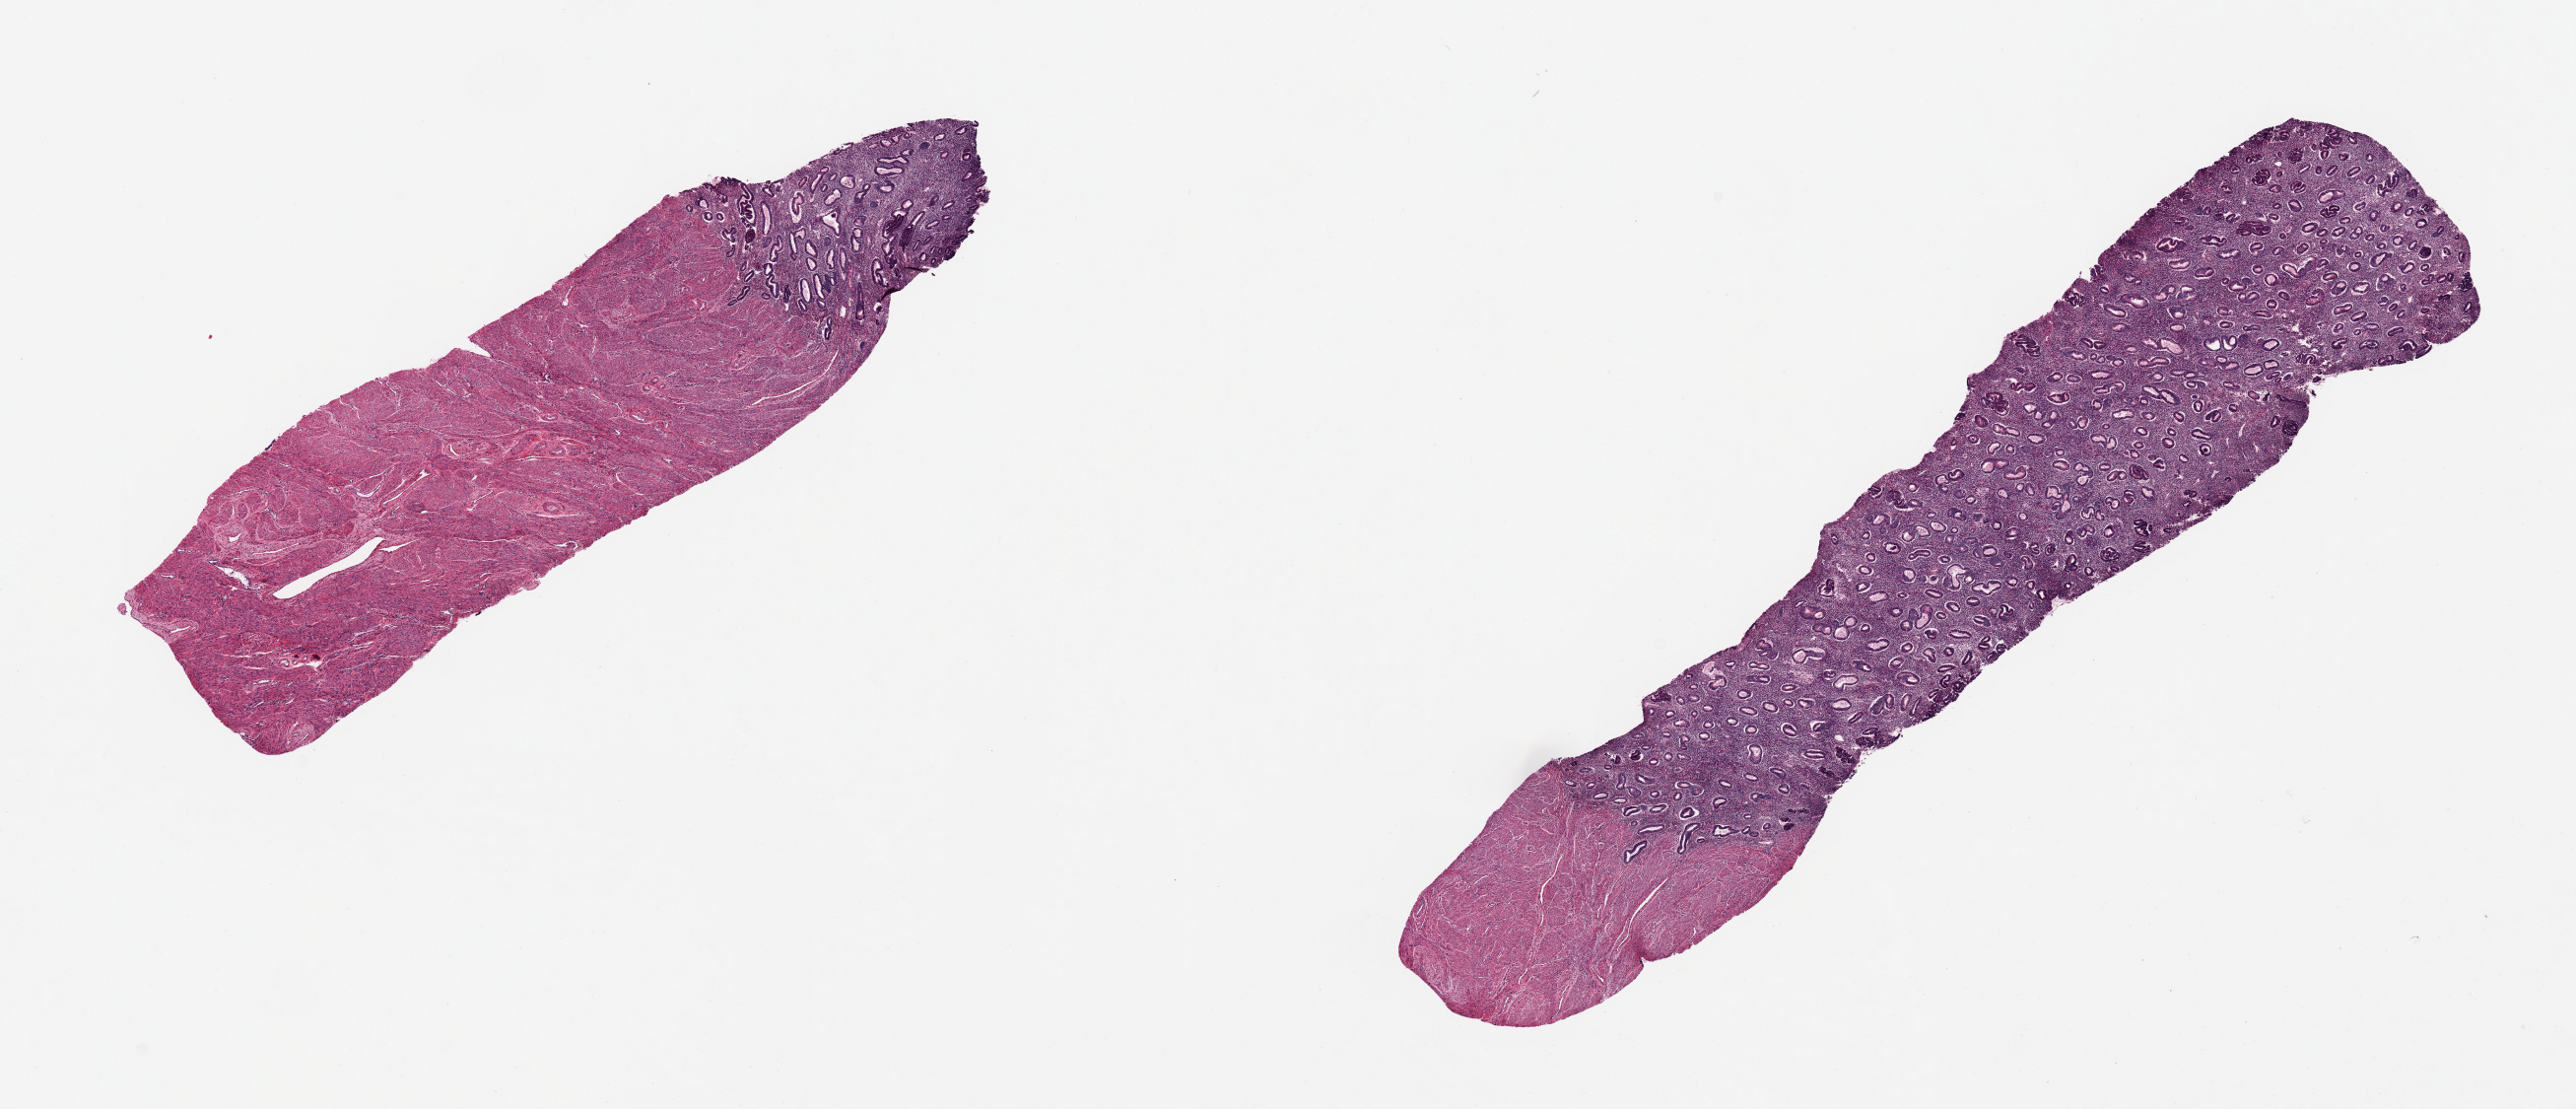
Digitized hematoxylin and eosin (H&E)-stained section, whole scanned area (about 20.7 x 8.9 mm, acquisition: 20x scan) shown as a low-resolution overview. PAXgene-fixed, paraffin-embedded tissue. Sampled site (target tissue): uterus. Donor tissue sample. Female donor.
• pathologist's review note for this sample: 2 pieces: 10x2mm with abundant endometrium; 7.6x2 with little endometrium